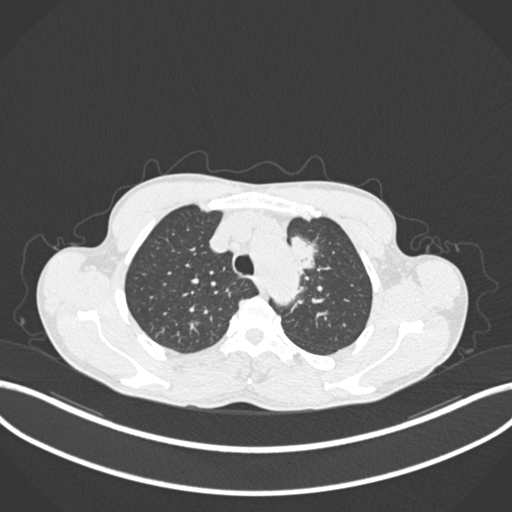
Chest CT, one axial slice; 120 kVp; lung window (W 1500 / L -600 HU); 1 mm slice thickness; 512 × 512 image matrix, field of view 400 × 400 mm. Patient: male, 58 years. Case-level facts recorded for this patient, not image findings: clinical TNM (as recorded): T1c N1 M0.
Annotated regions visible in this slice (rectangle marked by the reading radiologist):
- lung tumour (recorded histology: adenocarcinoma): bounding box <288,233,316,279> (left, top, right, bottom; pixels)